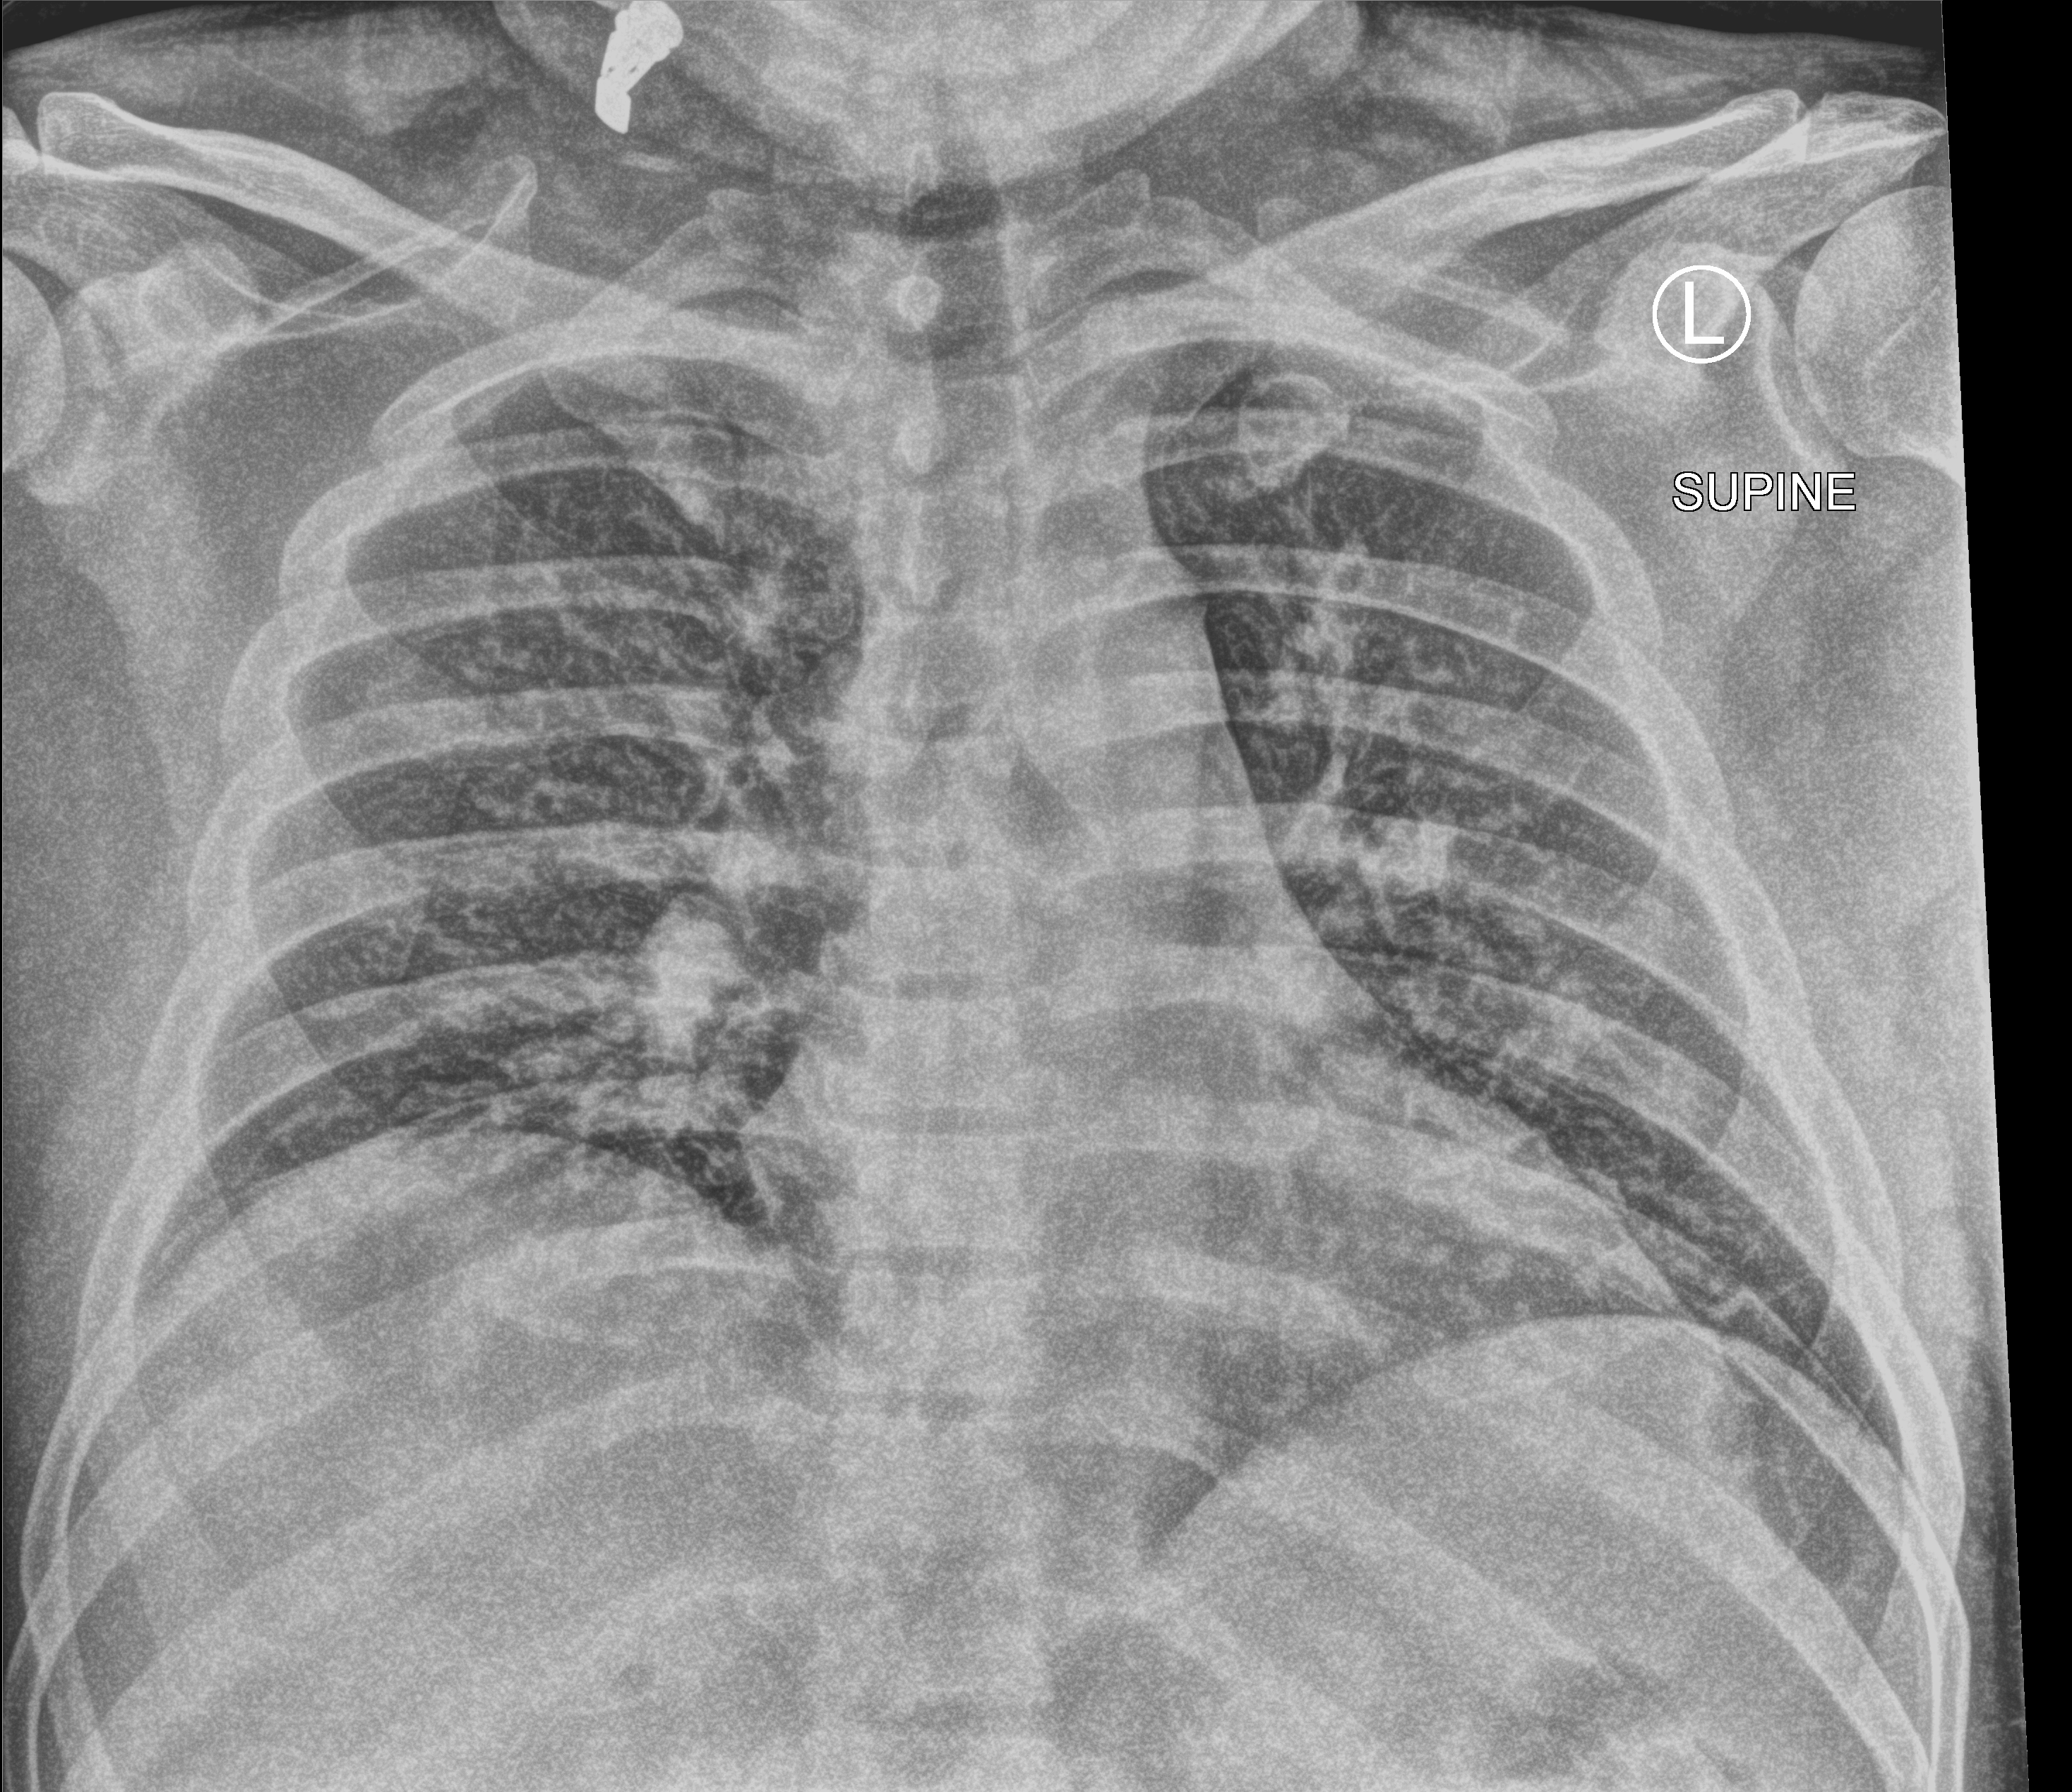
Bedside chest radiograph (computed radiography), anteroposterior (AP) projection. Patient hospitalised with COVID-19; male, aged 18–59 years.
From the hospital-stay record, not from the radiograph (when in the stay this image was taken is not recorded):
- admitted to intensive care during this hospital stay: no